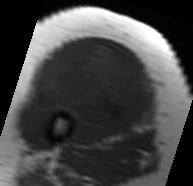
MRI of an extremity soft-tissue mass, one axial slice. Slice 36 of 91 in the series (ordered by position). MR volume resampled by the dataset authors to the PET/CT grid (not the native acquisition matrix). 3.27 mm slice thickness. 193 × 186 image matrix. Female patient. From the clinical record (not read from this slice): histological type: malignant solitary fibrous tumor; grade: intermediate; site of the primary tumour: right thigh.
Outlined on this slice (expert contour drawn on MRI and transferred to this co-registered scan by the dataset authors):
- gross tumour volume including surrounding oedema: bounding box [x1, y1, x2, y2] px = [29, 40, 151, 134]
- gross tumour volume (mass): [35, 40, 148, 130]